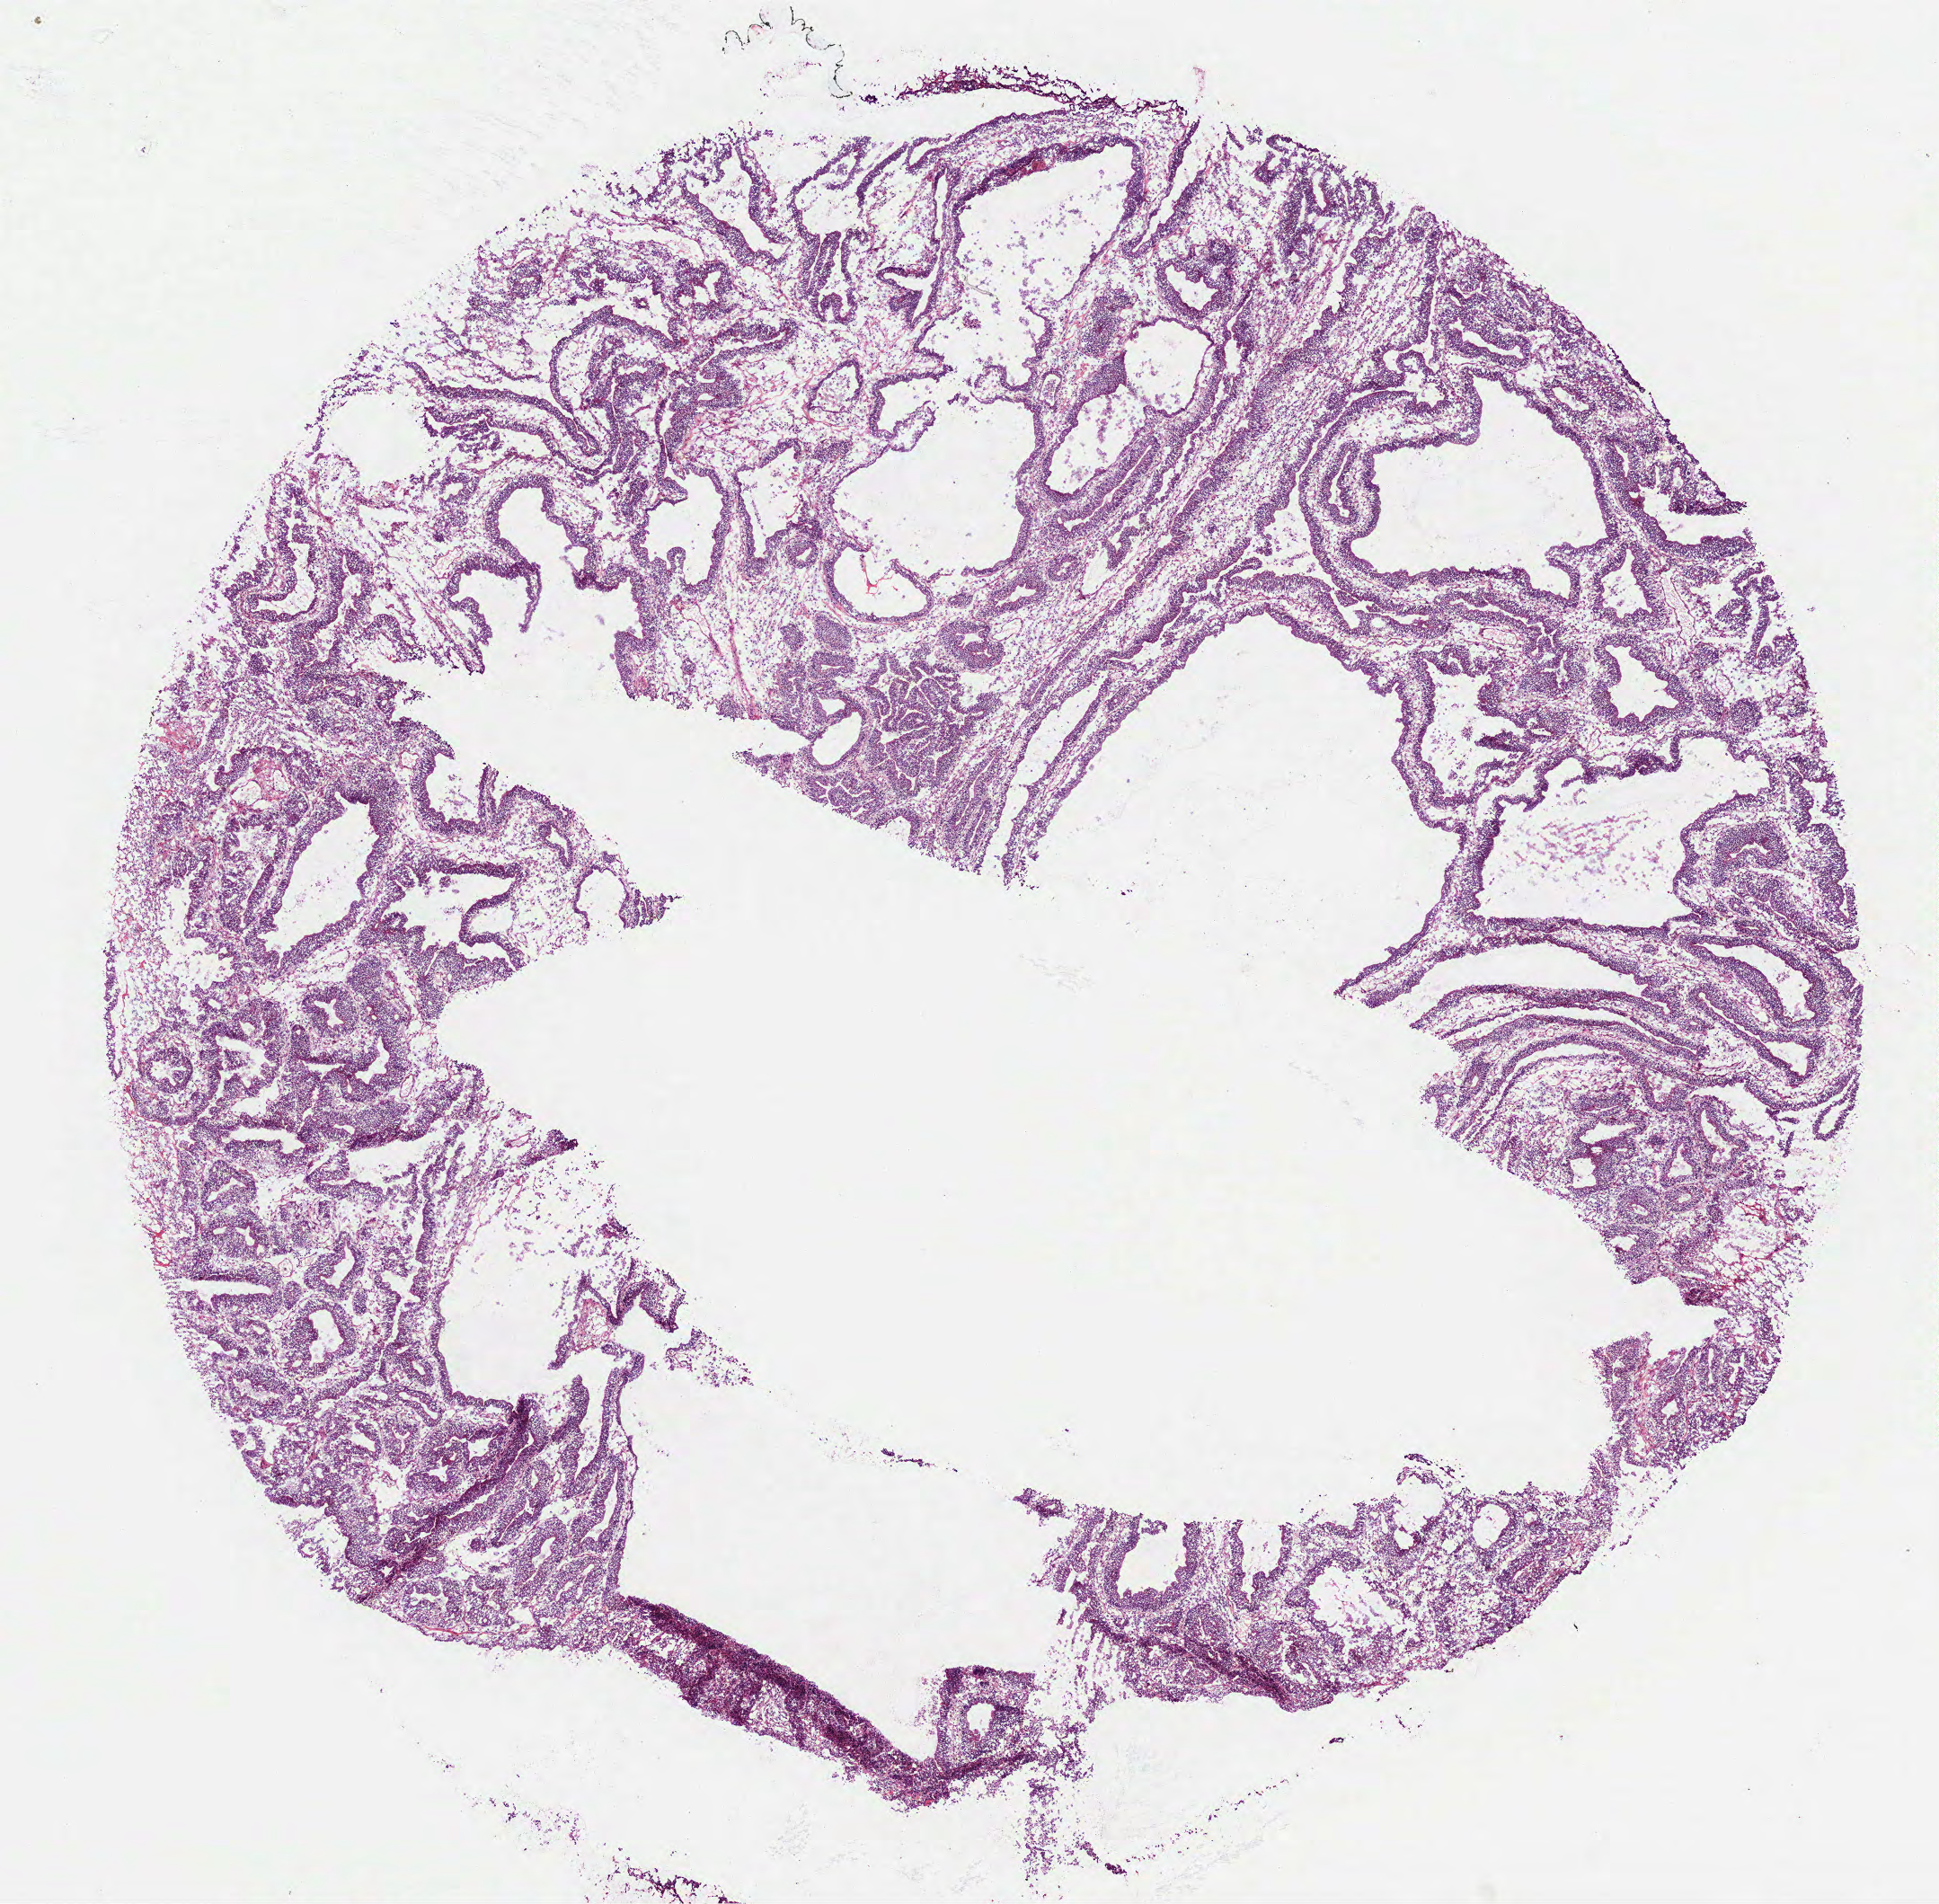
Whole-slide histology image, H&E-stained, shown as a low-resolution overview of the whole scanned area (about 8.7 x 8.5 mm, acquisition: 40x scan). Frozen section from the bottom of the tissue portion. Stomach, primary tumour sample. Patient sex: male. Histologic grade: G2 (moderately differentiated). Pathologist review of this section (percent, as recorded): tumour cells 100%, tumour nuclei 80%, normal cells 0%, stromal cells 0%, necrosis 0%. Infiltration values recorded for this section: lymphocyte infiltration 10%, monocyte infiltration 2%, neutrophil infiltration 5%.
• AJCC pathologic stage: IA (6th edition)
• lymph nodes positive (case pathology): 0 of 25 examined
• pathologic diagnosis: Adenocarcinoma, intestinal type